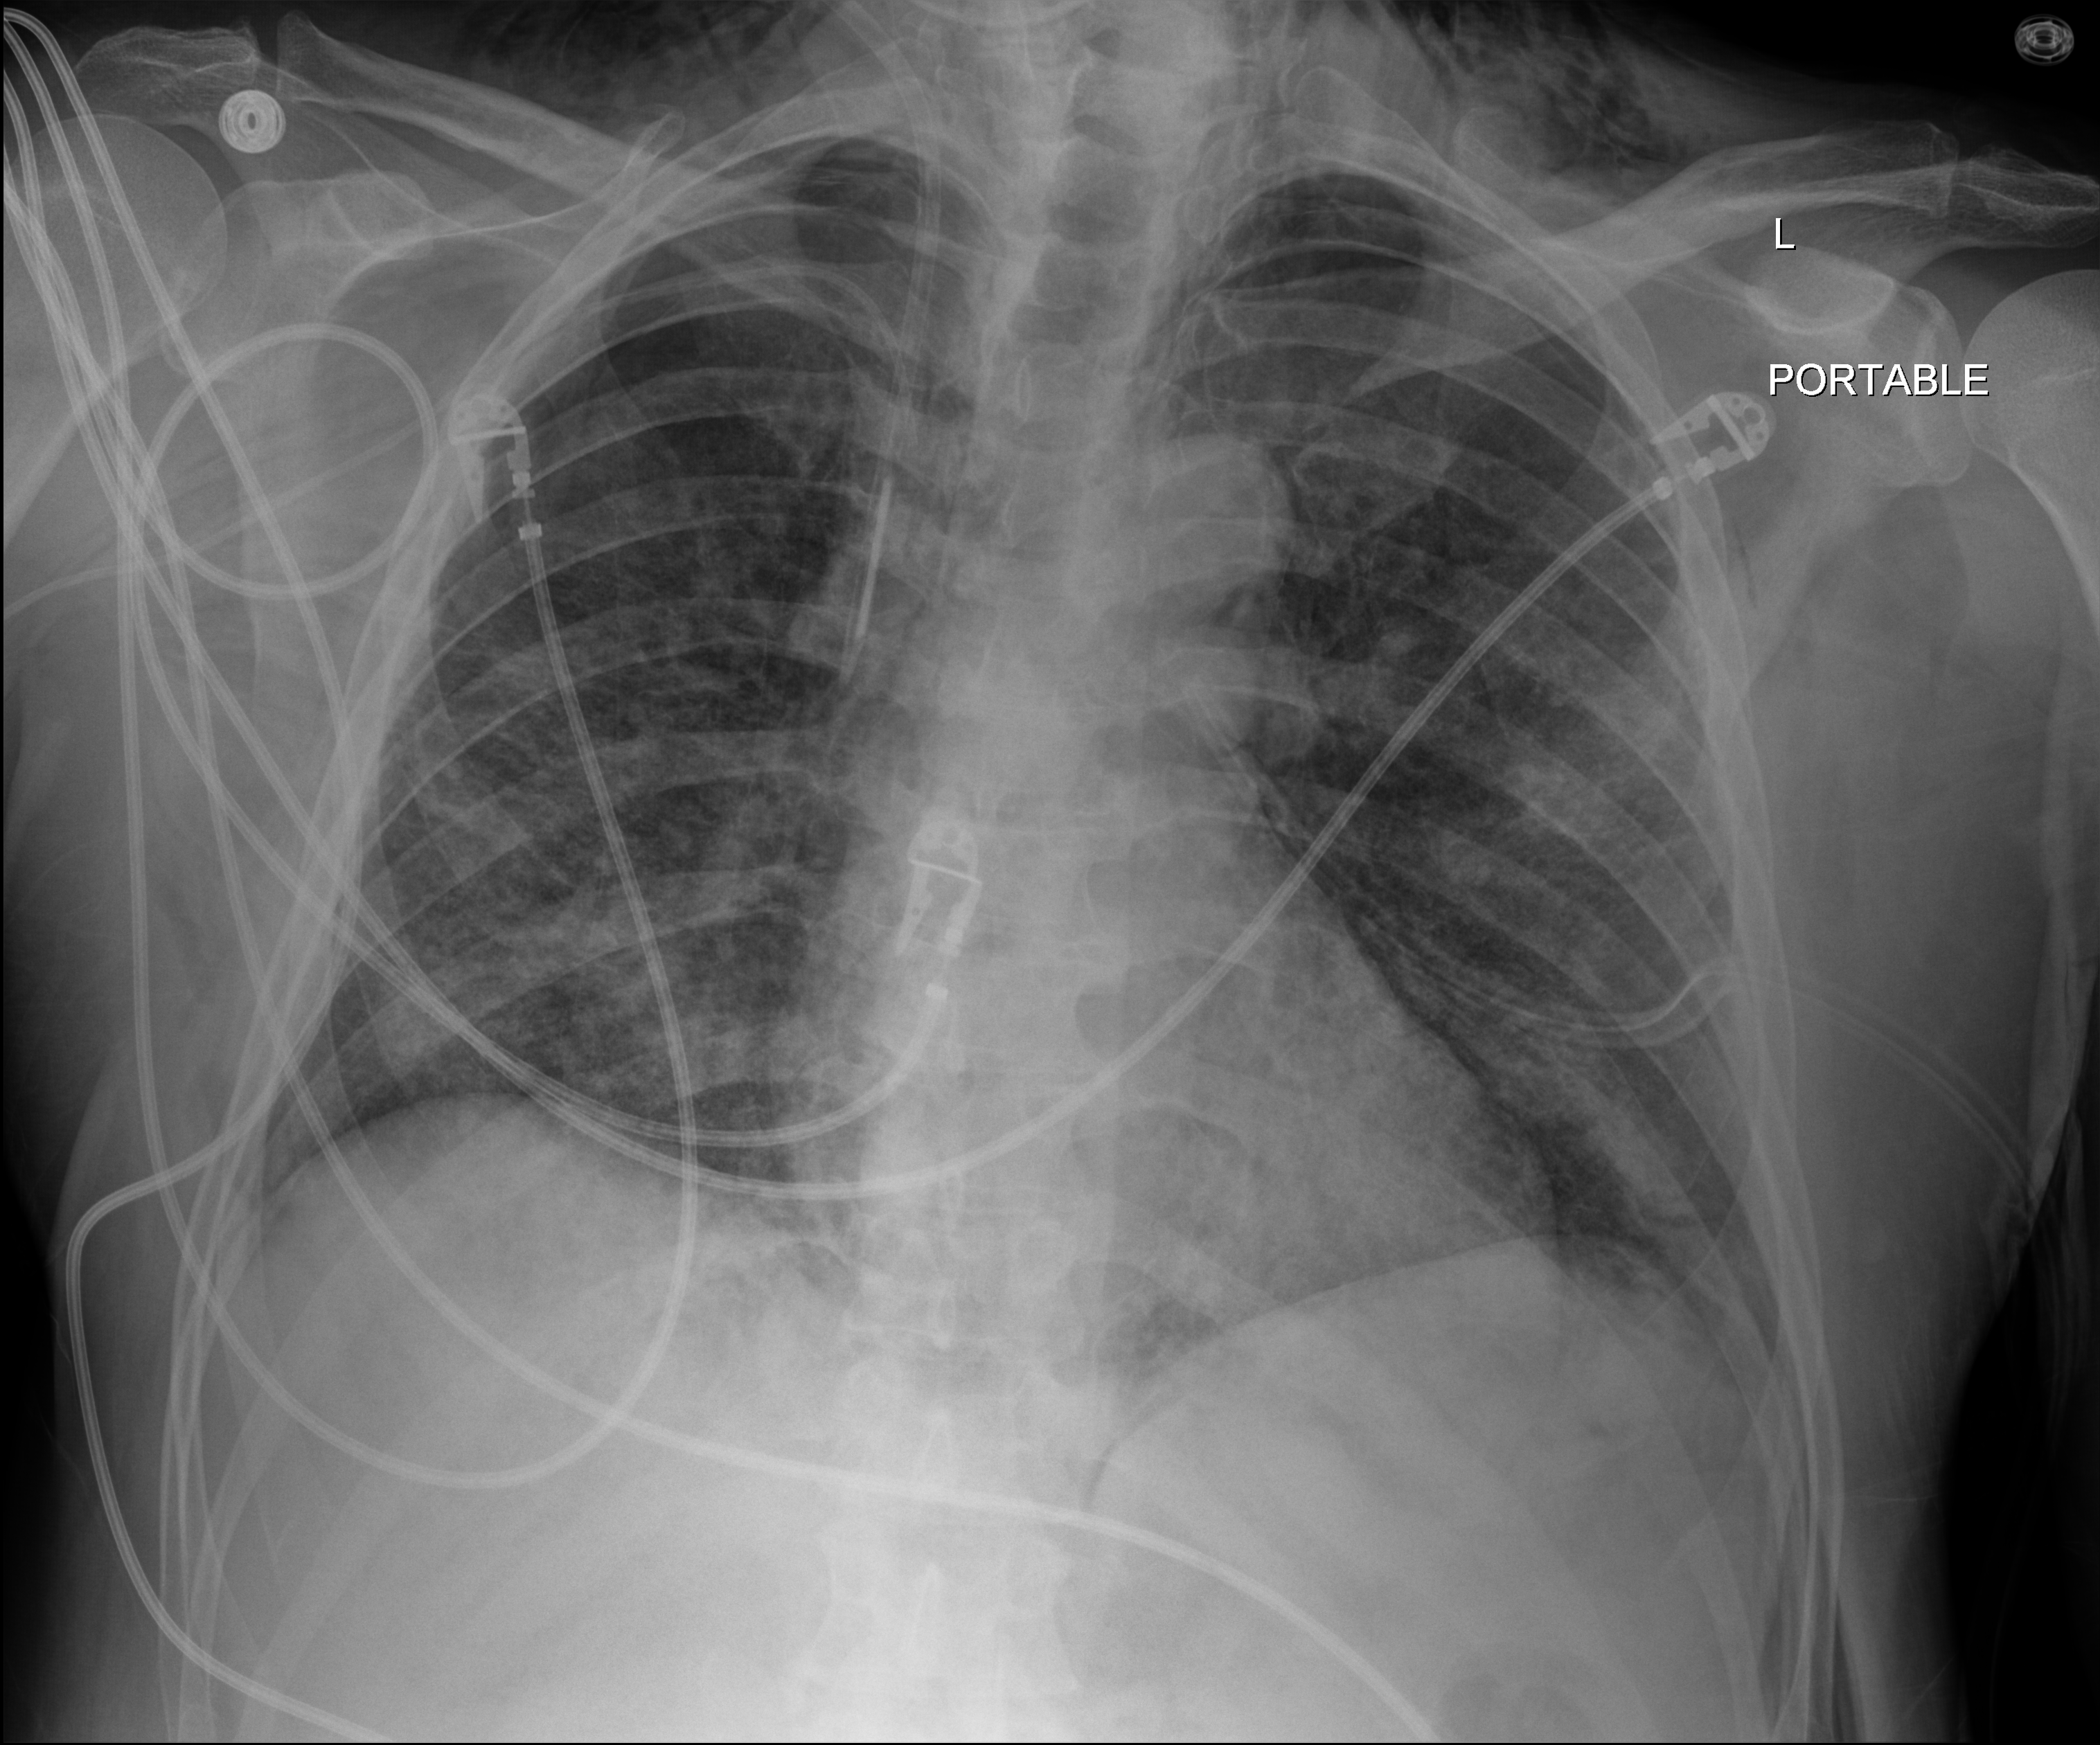
Bedside chest radiograph (digital radiography); anteroposterior (AP) projection. Male patient hospitalised with COVID-19, age 18–59 years.
Hospital-stay facts (about this admission, not read from this image; timing relative to this image not recorded):
- hypertension (admission record): no
- admitted to intensive care during this hospital stay: yes
- diabetes (admission record): no